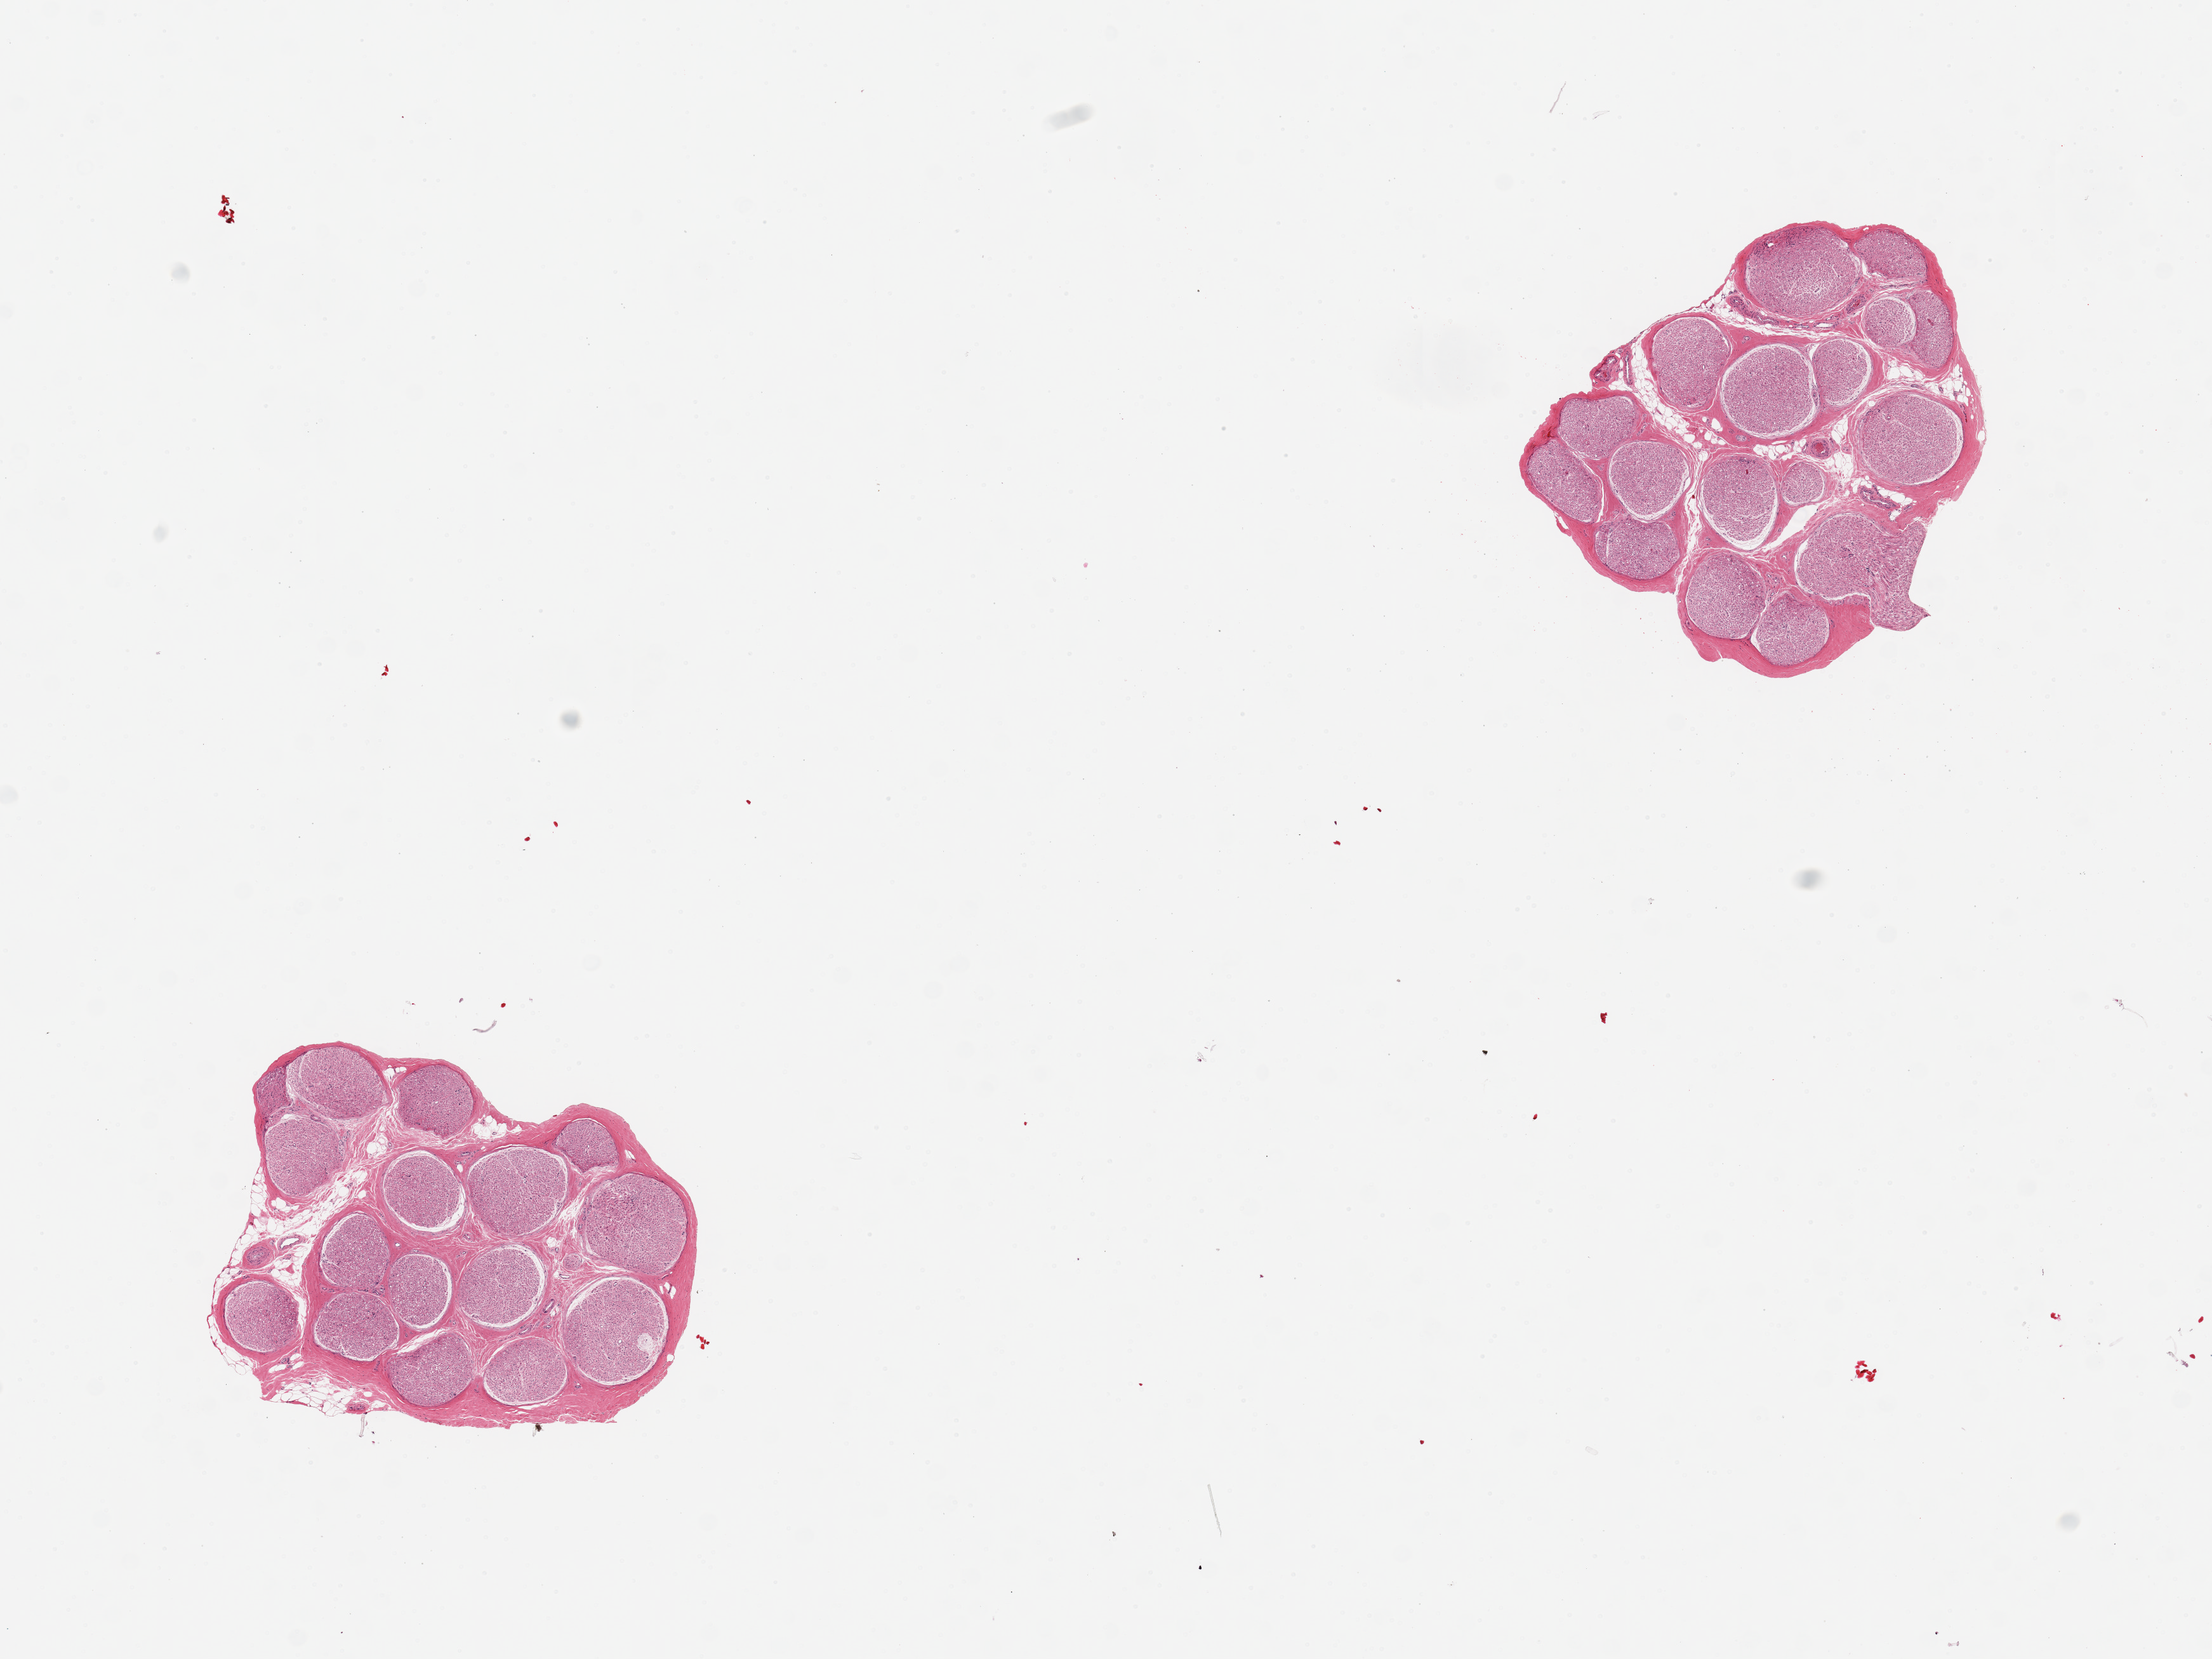
Haematoxylin and eosin whole-slide image — low-resolution overview of the scanned area, about 13.8 x 10.3 mm (from a 20x scan). PAXgene-fixed paraffin-embedded (PFPE) section. Target tissue: tibial nerve. Tissue donor sample. Donor: male.
Reviewer comment on this tissue sample: 2 pieces; 10% internal fat.